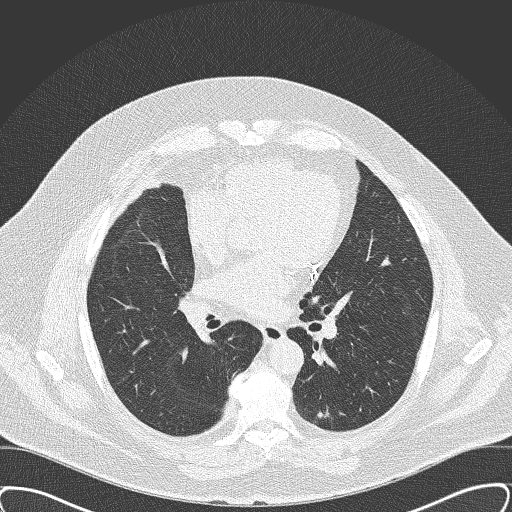
Axial slice from a low-dose chest CT screening exam, third screening round (two years after baseline), lung window (W 1500 / L -600 HU), lung (sharp) reconstruction kernel (B50f), slice 90 of 161 in the series. Male participant, aged 63 years at enrolment. Former smoker at enrolment.
Expert-annotated lung lesion, bounding box <302,390,355,434> (left, top, right, bottom; pixels). The screening reader recorded 2 non-calcified nodules or masses ≥4 mm on this exam (left lower lobe, left lower lobe); which of them this box marks is not recorded. Later outcome: lung cancer diagnosed 47 days after this screen — squamous cell carcinoma, NOS, left lower lobe, moderately differentiated (G2), stage IA (AJCC 6th edition), 15 mm at pathology.